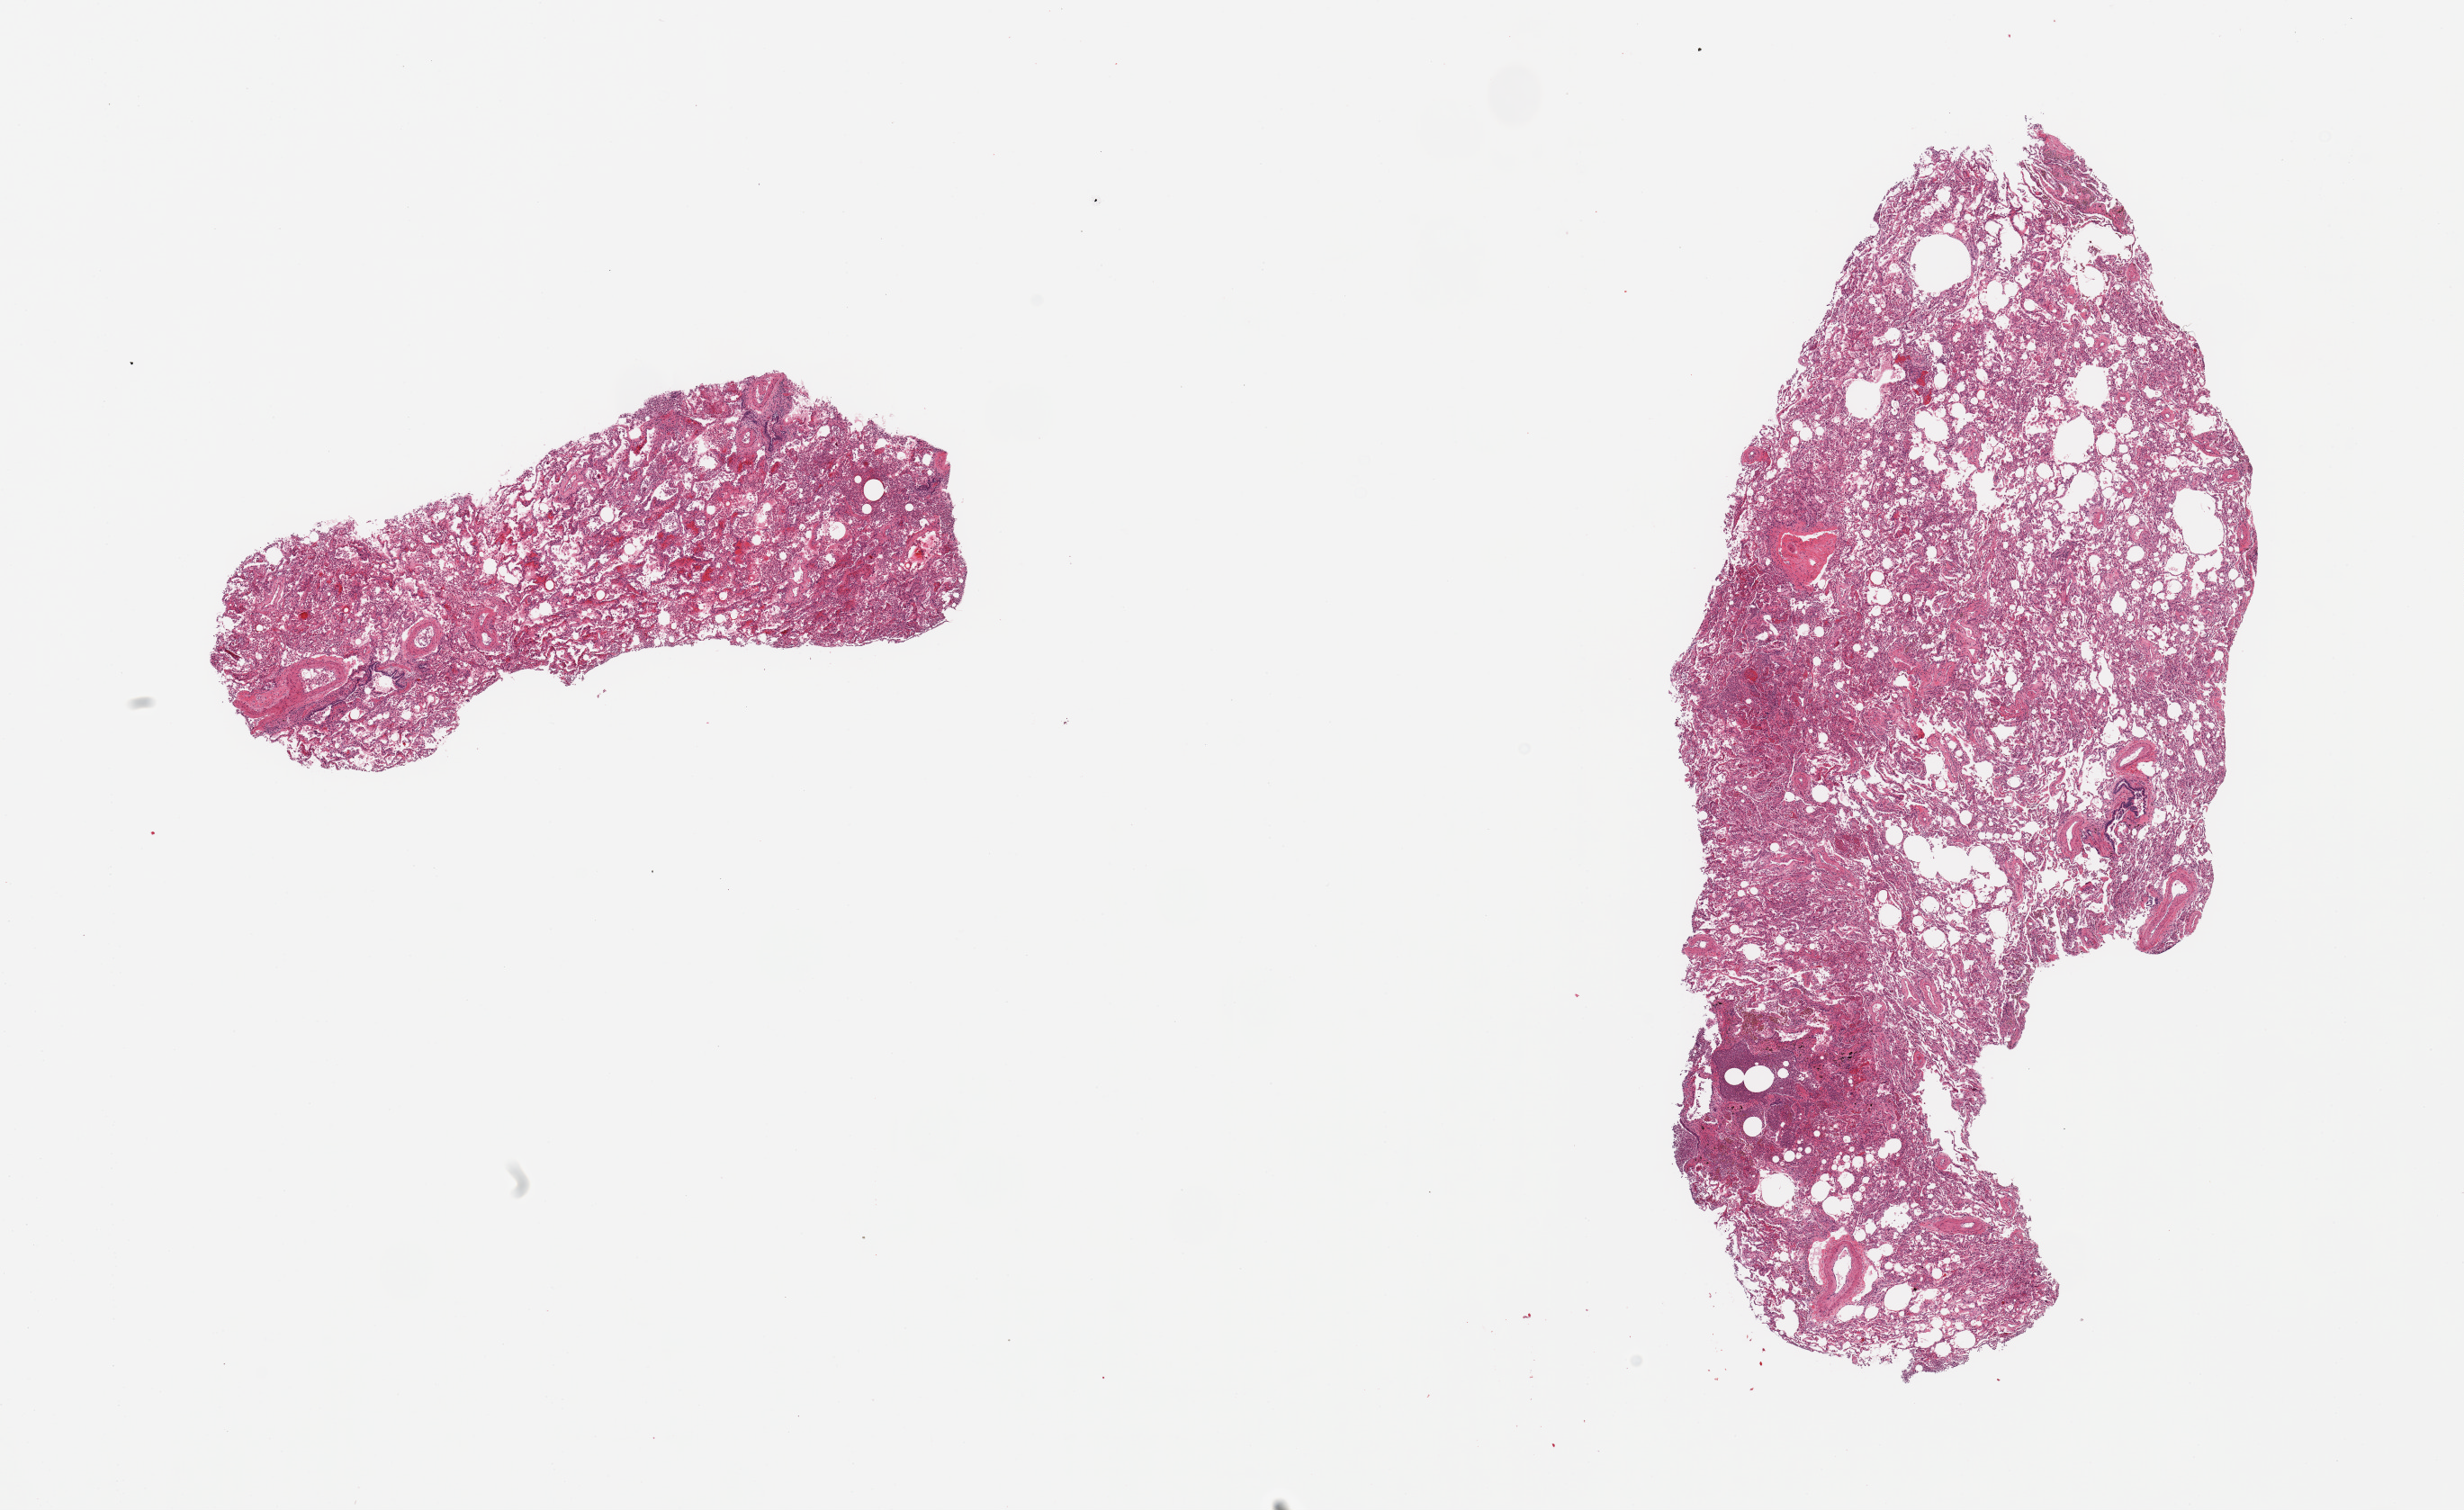
Whole-slide image, H&E stain — a low-resolution overview of the entire scanned area, about 21.7 x 13.3 mm (from a 20x scan); PAXgene-fixed, paraffin-embedded tissue; sampled site (target tissue): lung; donor tissue sample.
Pathologist's review note for this sample: 2 pieces; 60 & 50% bronchopneumonia; patchy emphysema.